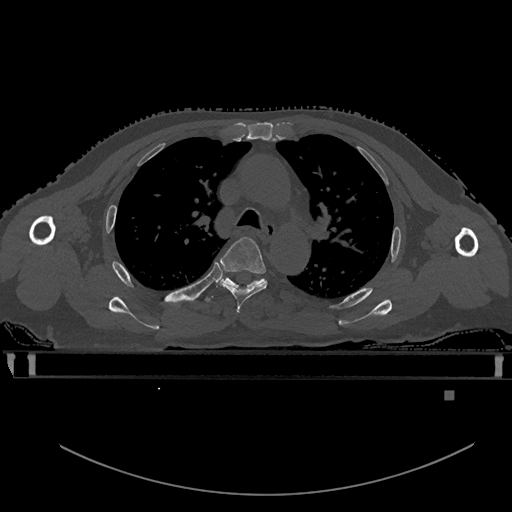
CT including the spine, one axial slice; position 392 of 969 along the scan axis; bone window (W 1800 / L 400 HU); 0.5 mm slice thickness; 512 × 512 image matrix, field of view 456 × 456 mm. Patient: male, 82 years. Case-level facts recorded for this patient, not image findings: primary cancer: prostate.
Outlined on this slice (semi-automatic segmentation, software-assisted and operator-edited):
- T4 vertebra: bounding box (x1, y1, x2, y2) in pixels: (220, 236, 268, 312)
- T5 vertebra: (204, 271, 265, 302)